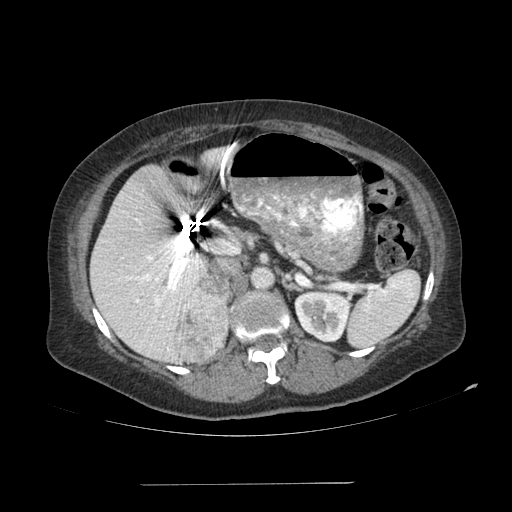
Contrast-enhanced abdominal CT, one axial slice. Reconstruction kernel SOFT. 120 kVp. Soft-tissue window (W 400 / L 40 HU). 2.5 mm slice thickness. 512 × 512 image matrix, field of view 440 × 440 mm. Patient: female, 67 years. From the clinical record (not read from this slice): diagnosis: adrenocortical carcinoma; tumour side: right adrenal; tumour size at pathology: 9.8 cm.
Annotated regions visible in this slice (semi-automatic segmentation, software-assisted and operator-edited):
- mass: bounding box [x1, y1, x2, y2] px = [175, 276, 232, 361]